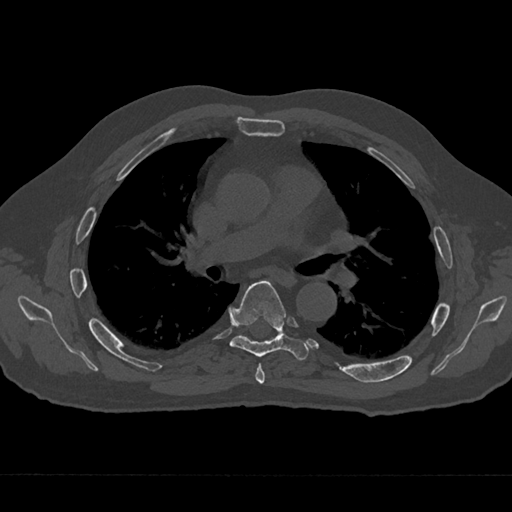
CT including the spine, one axial slice; slice 424 of 797 in the series (ordered by position); reconstruction kernel Br40s/3; 120 kVp; bone window (W 1800 / L 400 HU); 512 × 512 image matrix, field of view 377 × 377 mm. Patient: male, 75 years. Case-level facts recorded for this patient, not image findings: primary cancer: renal; vertebrae with lytic lesions (as recorded): T4.
Outlined on this slice (semi-automatic segmentation, software-assisted and operator-edited):
- T5 vertebra: bounding box <255,363,265,384> (left, top, right, bottom; pixels)
- T6 vertebra: <230,281,308,361>